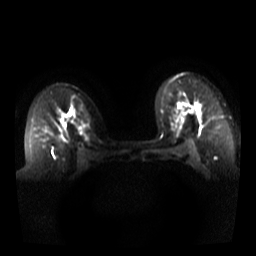
Breast MRI, one axial slice. Slice 23 of 44 in the series (ordered by position). Diffusion-weighted series; image 2 of 4 stored at this slice position (different b-values; order by instance number). 3 T. 5 mm slice thickness. 256 × 256 image matrix, field of view 340 × 340 mm. Female patient.
Outlined on this slice (outlined manually by an expert reader):
- tumour on diffusion-weighted imaging: bounding box [x1, y1, x2, y2] px = [178, 104, 182, 109]